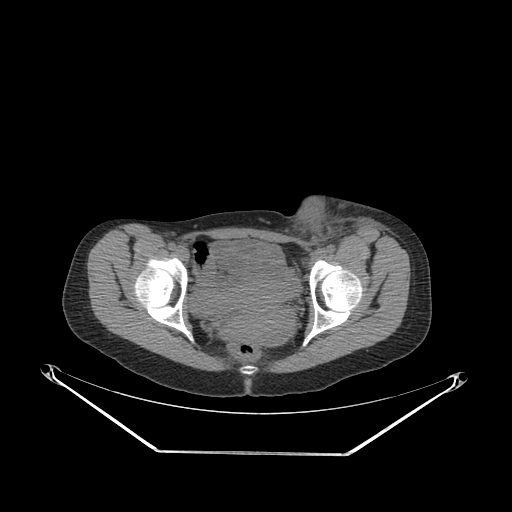
CT of an extremity soft-tissue mass (from a PET/CT study), one axial slice. Position 74 of 267 along the scan axis. Soft-tissue window (W 400 / L 40 HU). 512 × 512 image matrix, field of view 500 × 500 mm. Female patient. From the clinical record (not read from this slice): histological type: leiomyosarcoma; grade: high; site of the primary tumour: groin.
Outlined on this slice (expert contour drawn on MRI and transferred to this co-registered scan by the dataset authors):
- gross tumour volume including surrounding oedema: bounding box <283,199,387,255> (left, top, right, bottom; pixels)
- gross tumour volume (mass): <283,199,343,254>